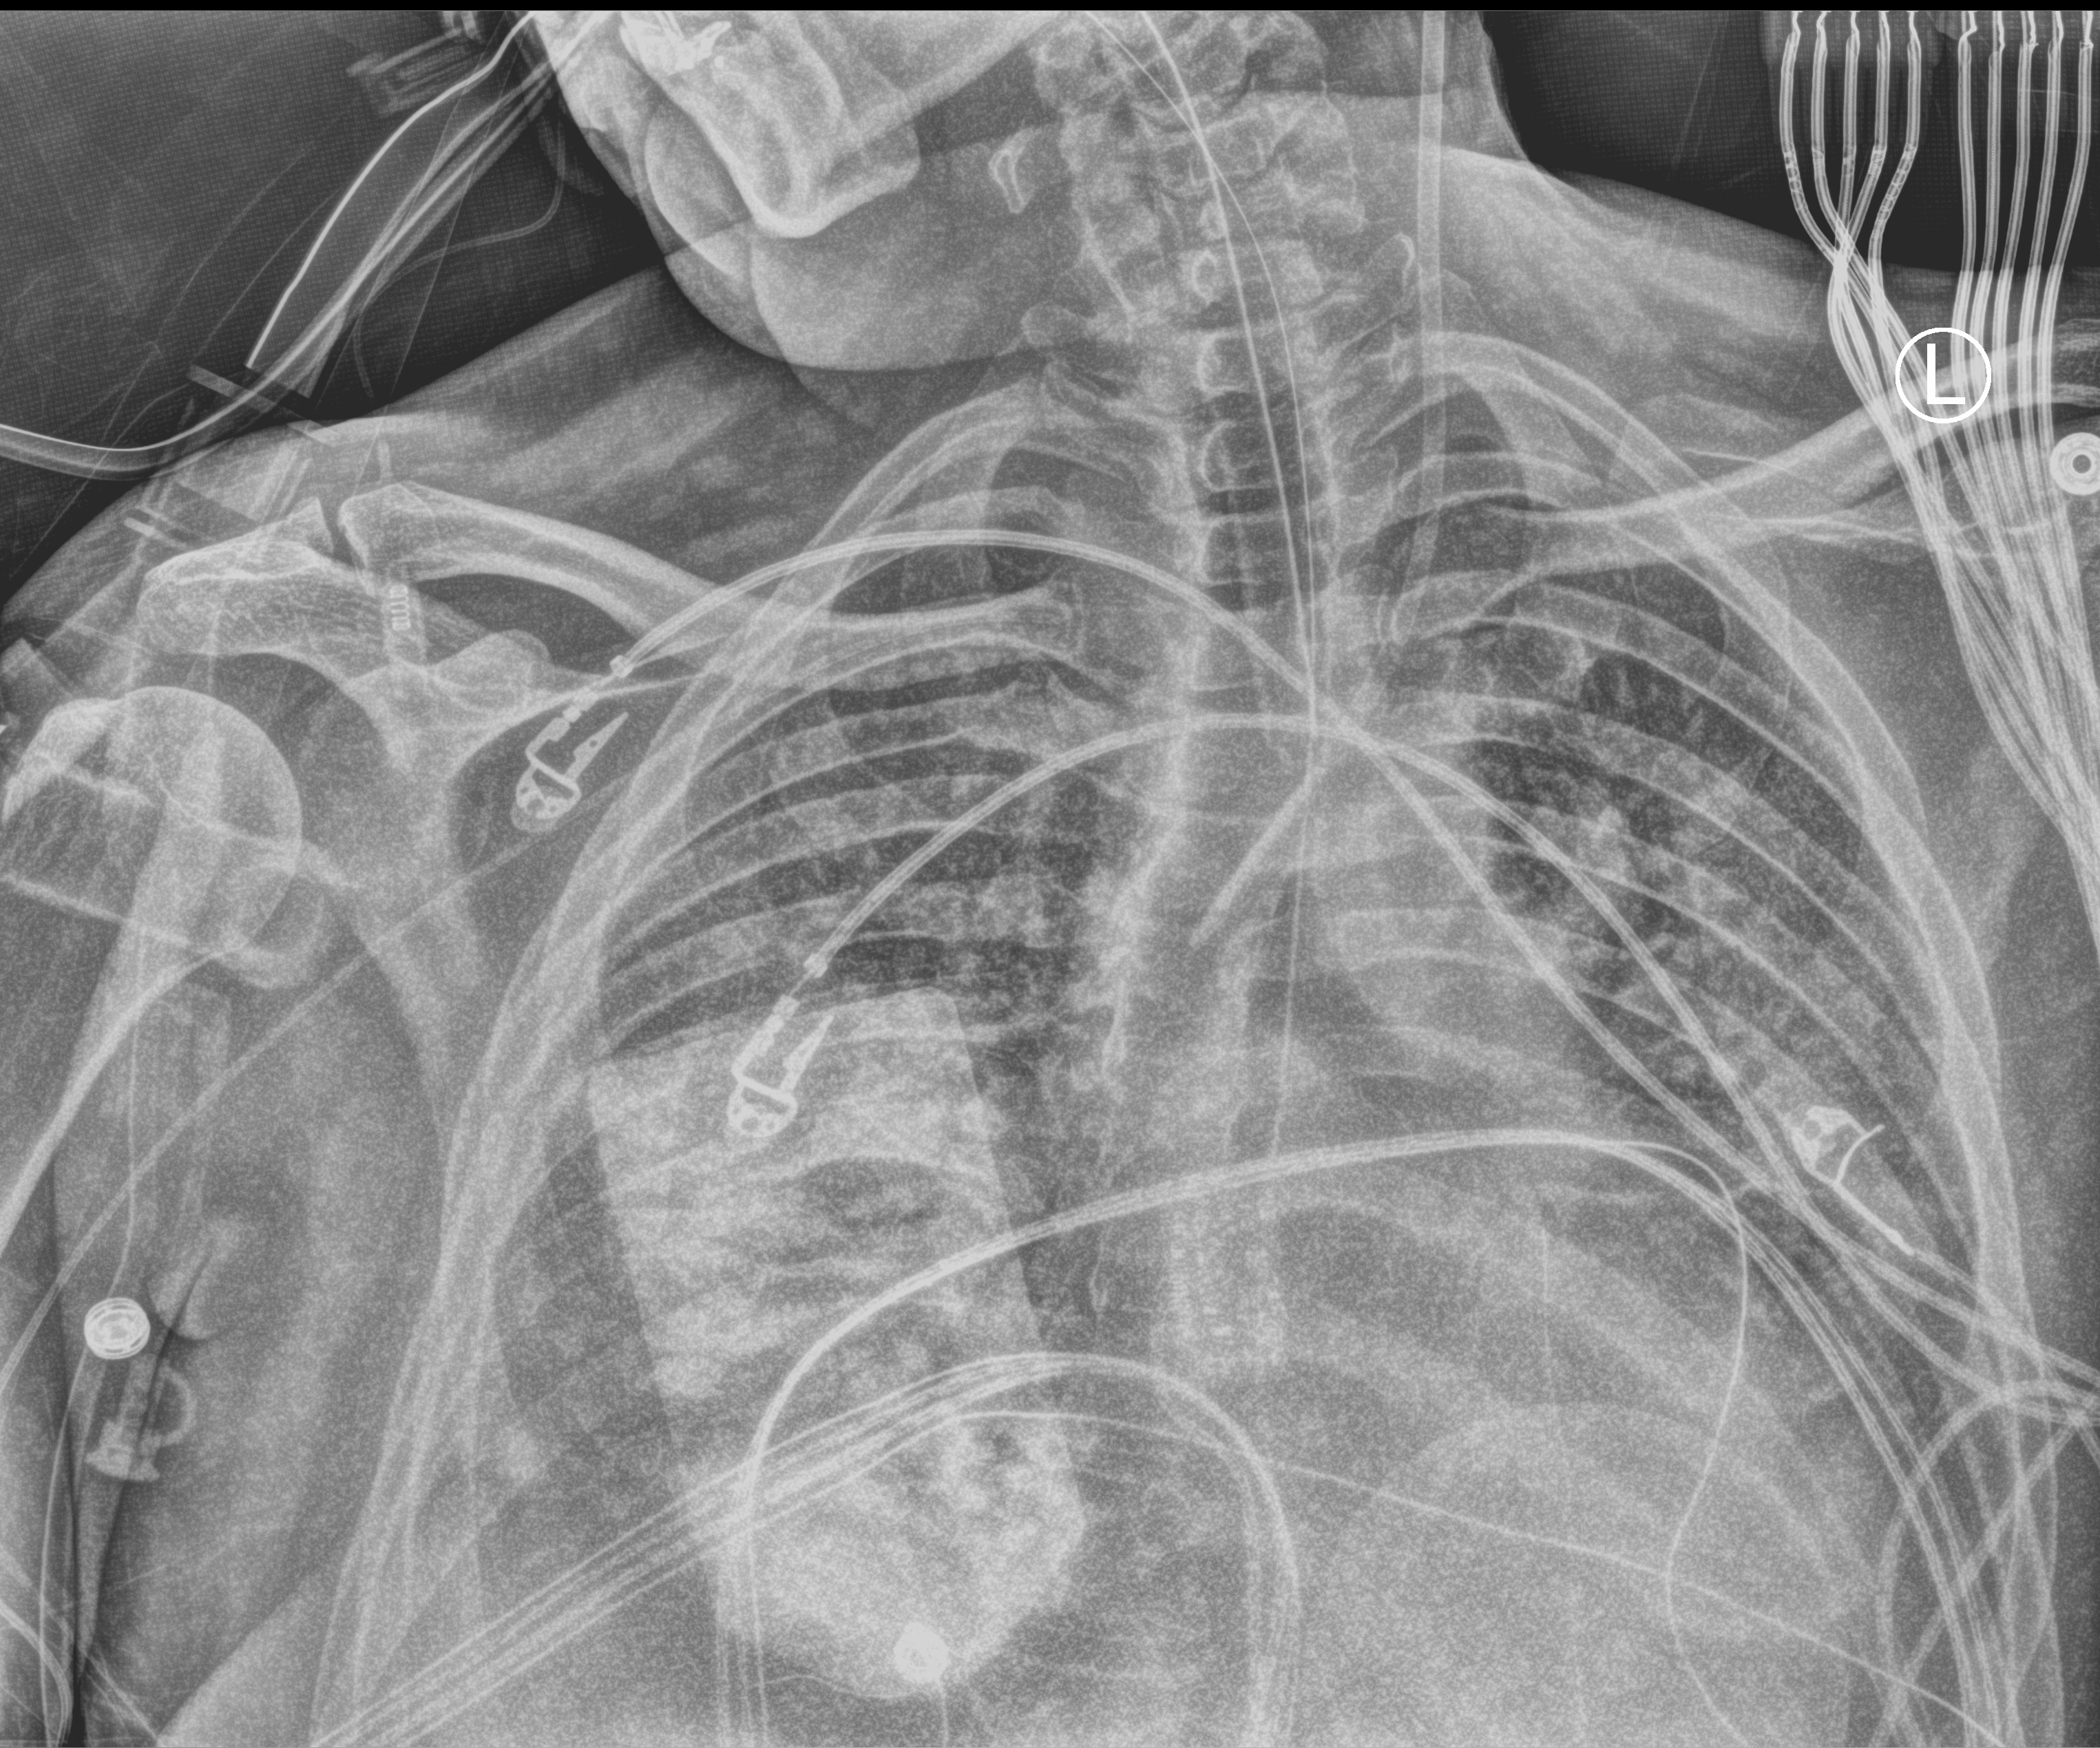
Bedside chest radiograph (computed radiography). Male patient hospitalised with COVID-19, age 18–59 years.
From the hospital-stay record, not from the radiograph (when in the stay this image was taken is not recorded): hypertension (admission record): no; COPD (admission record): no.